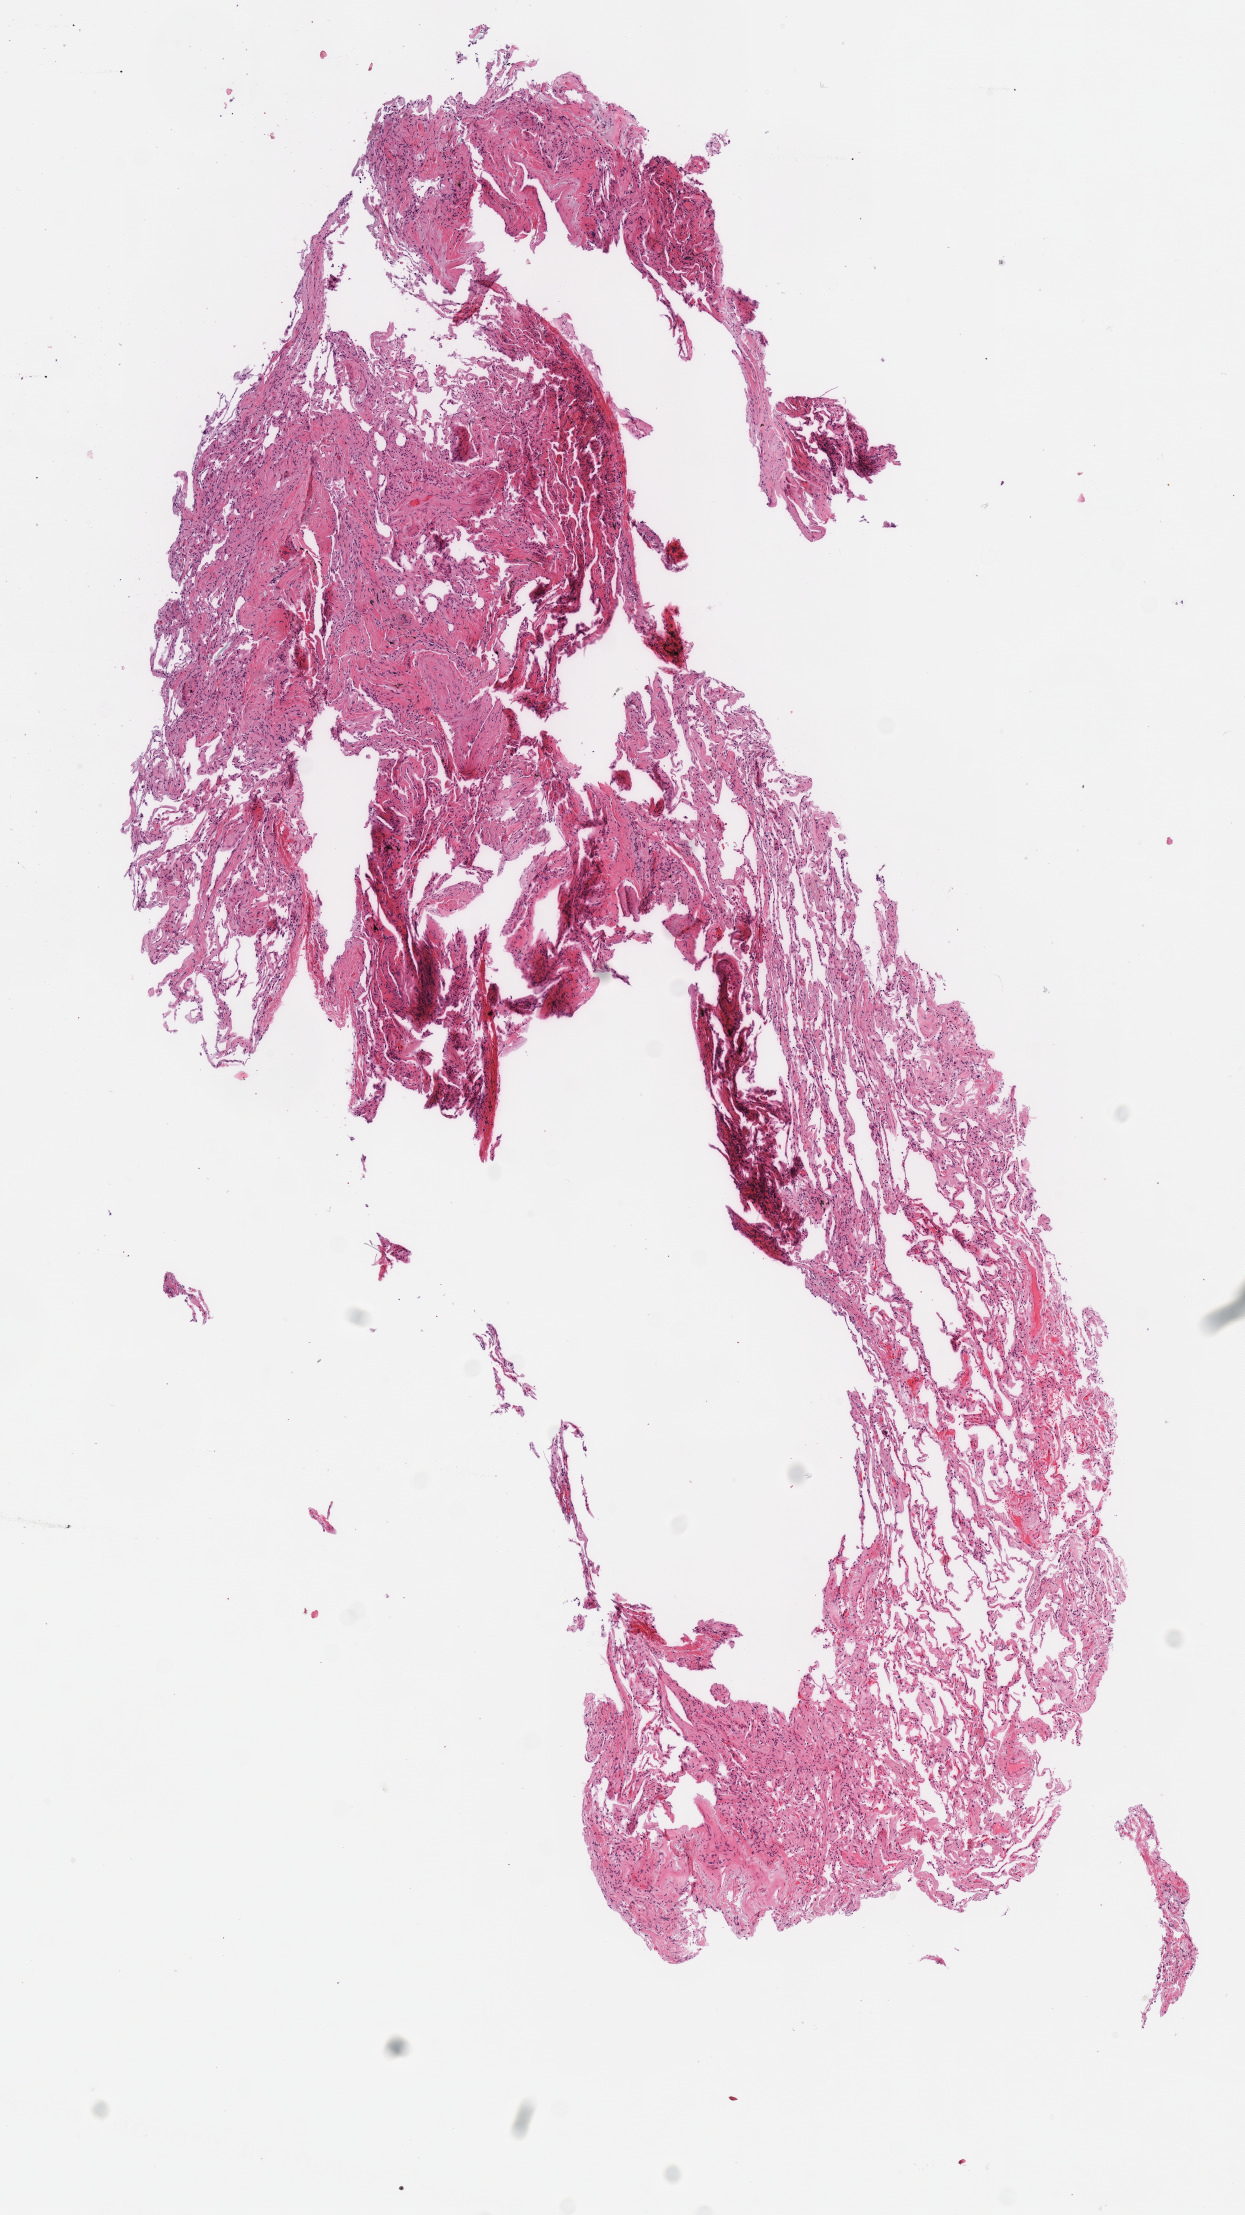
Hematoxylin and eosin (H&E) stained whole-slide image, low-resolution overview of the scanned area, about 4.9 x 8.7 mm (slide scanned at 40x), frozen section, sample: solid tissue normal (non-tumour tissue), lung. Female, age 74 years at initial diagnosis.
• this section: solid tissue normal (non-tumour) sample from the same patient
• patient diagnosis: Adenocarcinoma, NOS